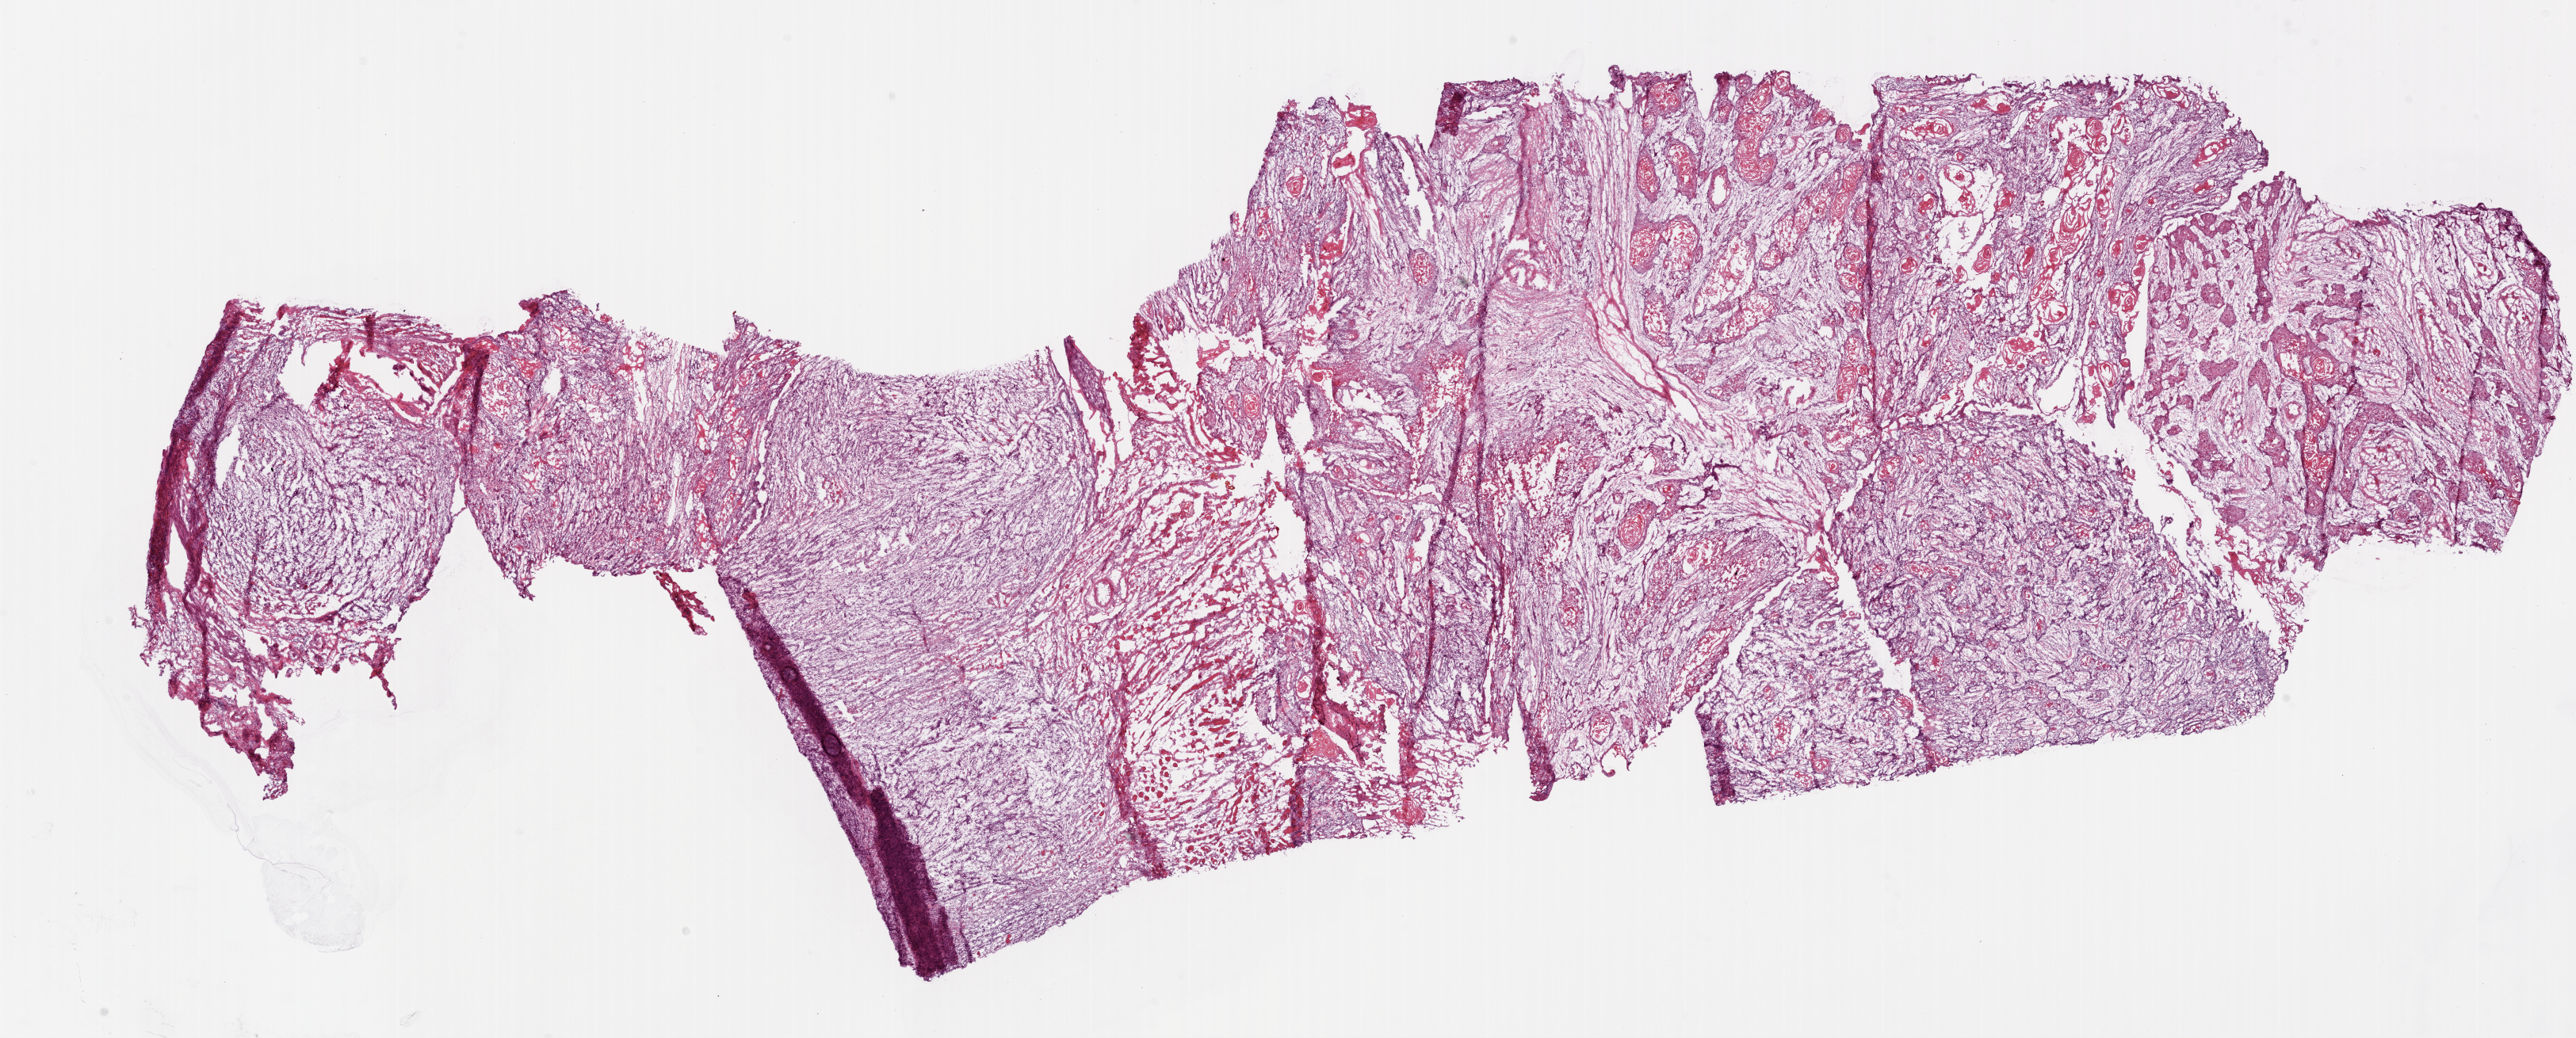
Hematoxylin and eosin (H&E) stained whole-slide image, shown as a low-resolution overview of the whole scanned area (about 26.1 x 10.5 mm); frozen section; sample: primary tumour, head and neck. Patient: male, age at initial diagnosis 78 years. Histologic grade: G3 (poorly differentiated). Composition of this section per pathologist review: tumour cells 85%, tumour nuclei 80%, normal cells 0%, stromal cells 15%, necrosis 0%.
- TNM: T3 N1 M0
- AJCC pathologic stage: III (6th edition)
- histologic diagnosis: Squamous cell carcinoma, NOS (tongue, NOS)